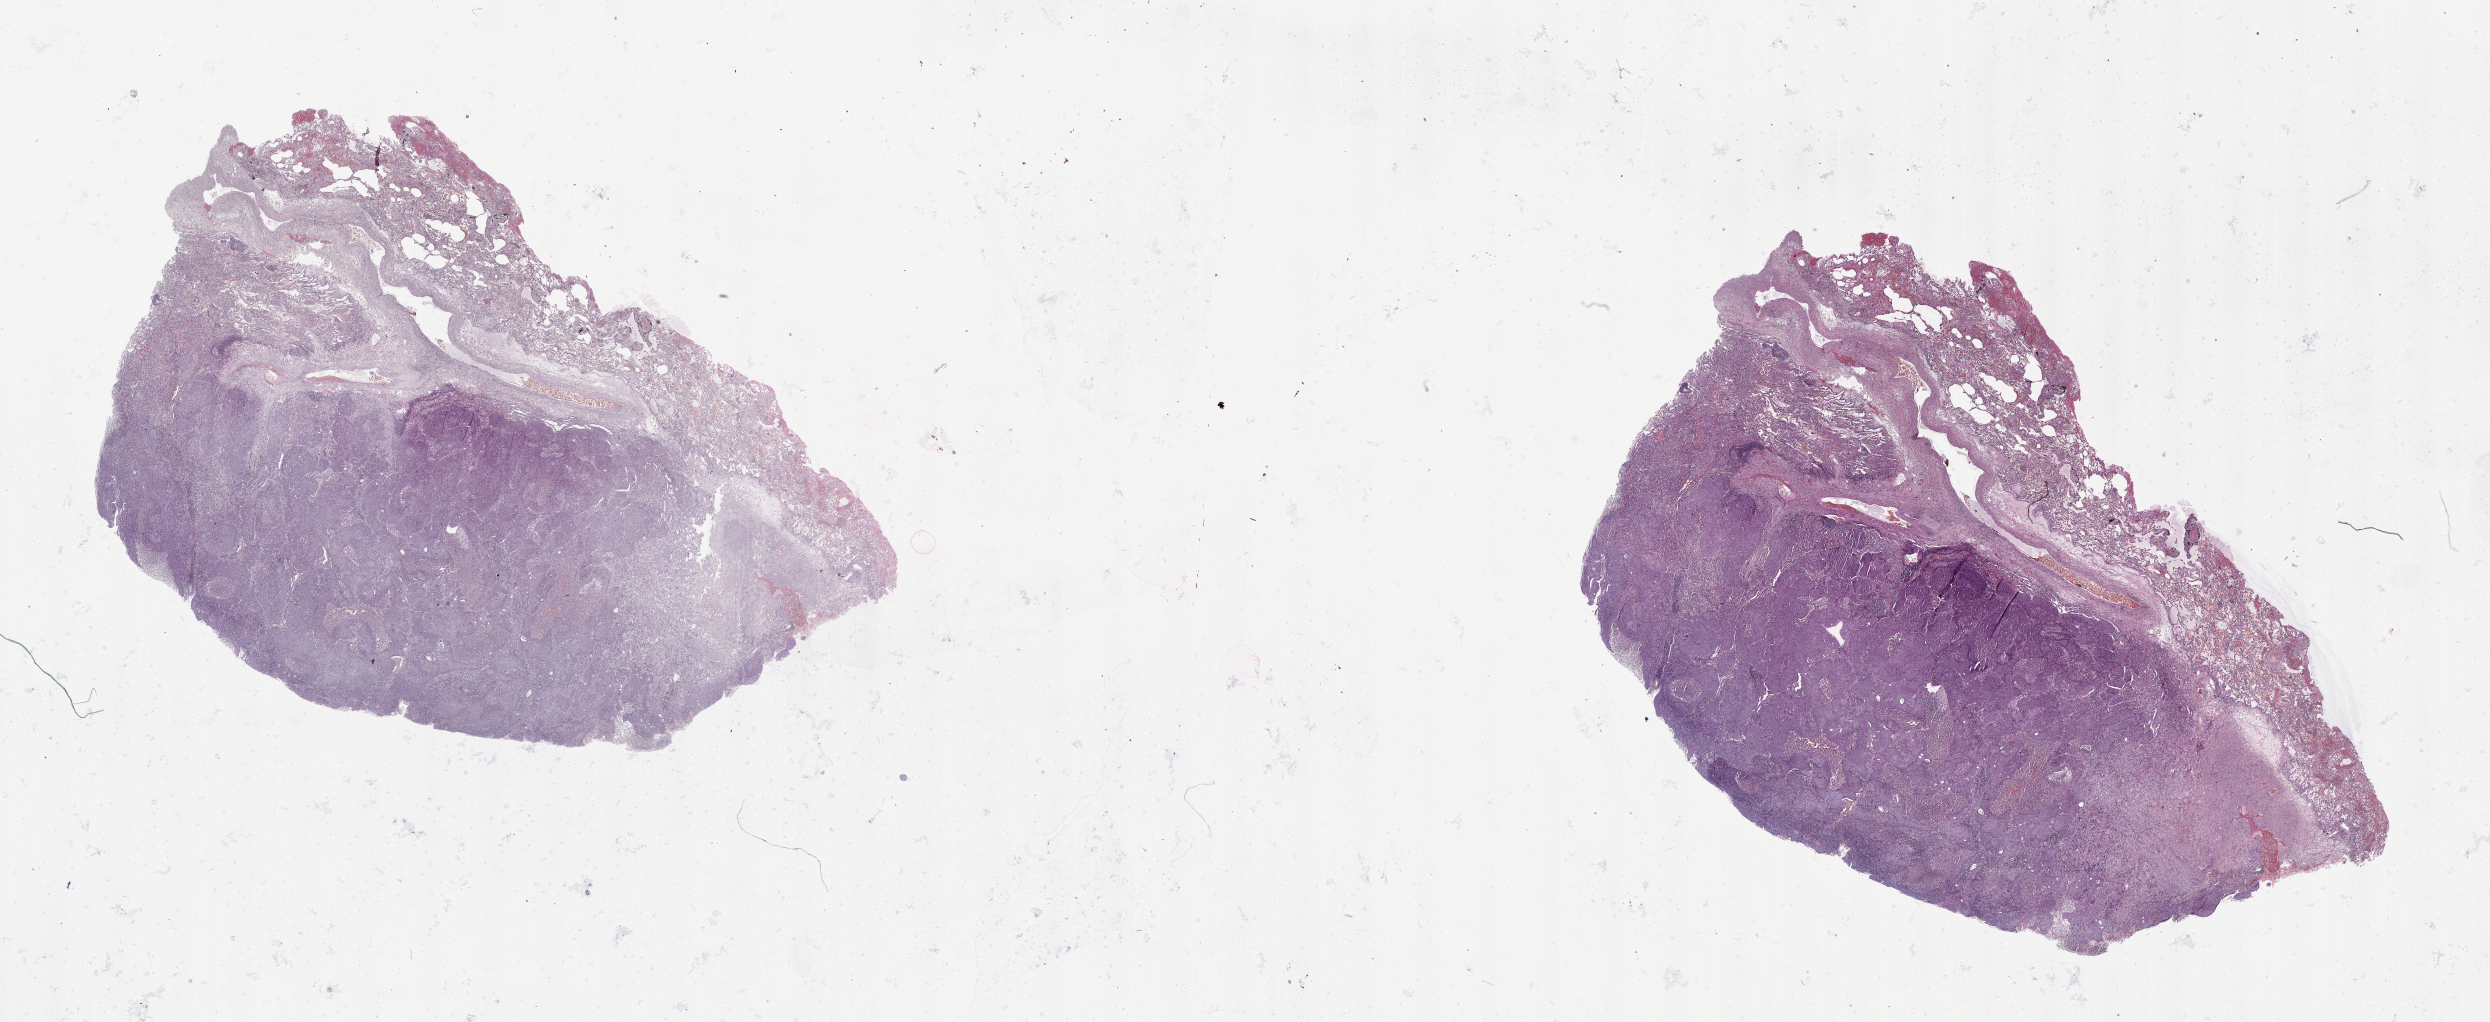
Digitized Hematoxylin and eosin (H&E) stained tissue section (whole slide), a low-resolution overview of the entire scanned area, about 40.1 x 16.5 mm. Lung, tumour tissue. Male, 75 y/o.
Patient diagnosis (cohort enrolment): squamous cell carcinoma (lung).